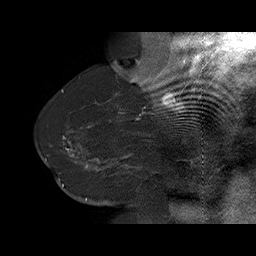
Breast MRI (dynamic contrast-enhanced), one sagittal slice; position 49 of 75 along the scan axis; dynamic contrast-enhanced series, time point 2 of 6 at this slice position (early post-contrast); 1.5 T; TE 4.5 ms, TR 32.4 ms; 3 mm slice thickness; 256 × 256 image matrix, field of view 180 × 180 mm. Female patient. From the clinical record (not read from this slice): setting: breast cancer imaged before/during neoadjuvant chemotherapy; receptor status: HR-positive, HER2-negative.
Annotated regions visible in this slice (semi-automatically segmented with operator editing):
- analysis volume of interest (the breast-tissue region the enhancement analysis was run in; not a lesion): box from (x=58, y=134) to (x=166, y=191) px
- tumour enhancement mask (voxels above the 100 % enhancement threshold inside the analysis volume of interest): (x=63, y=137)–(x=129, y=171)